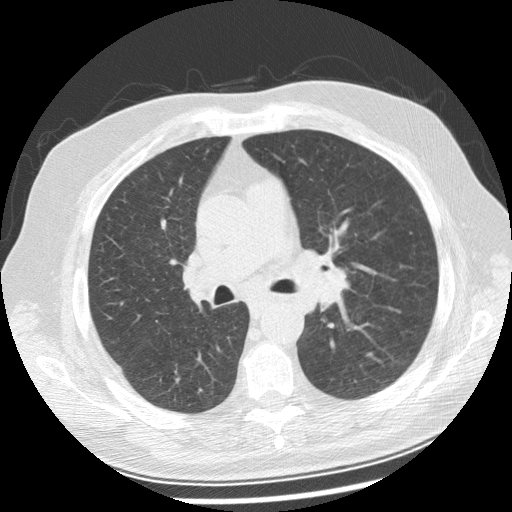
Axial slice from a low-dose chest CT screening exam, baseline annual screen, lung window (W 1500 / L -600 HU), 2.5 mm slice thickness, slice 102 of 250 in the series. Male participant, aged 70 years at enrolment.
Lesion marked by an expert reader, box from (x=281, y=242) to (x=363, y=309) px. Screening reader's record for this exam: no non-calcified nodule ≥4 mm recorded. Lung cancer was diagnosed 29 days after this screen: squamous cell carcinoma, keratinizing, NOS, left main stem bronchus, moderately differentiated (G2), stage IIIB (AJCC 6th edition), 40 mm at pathology.